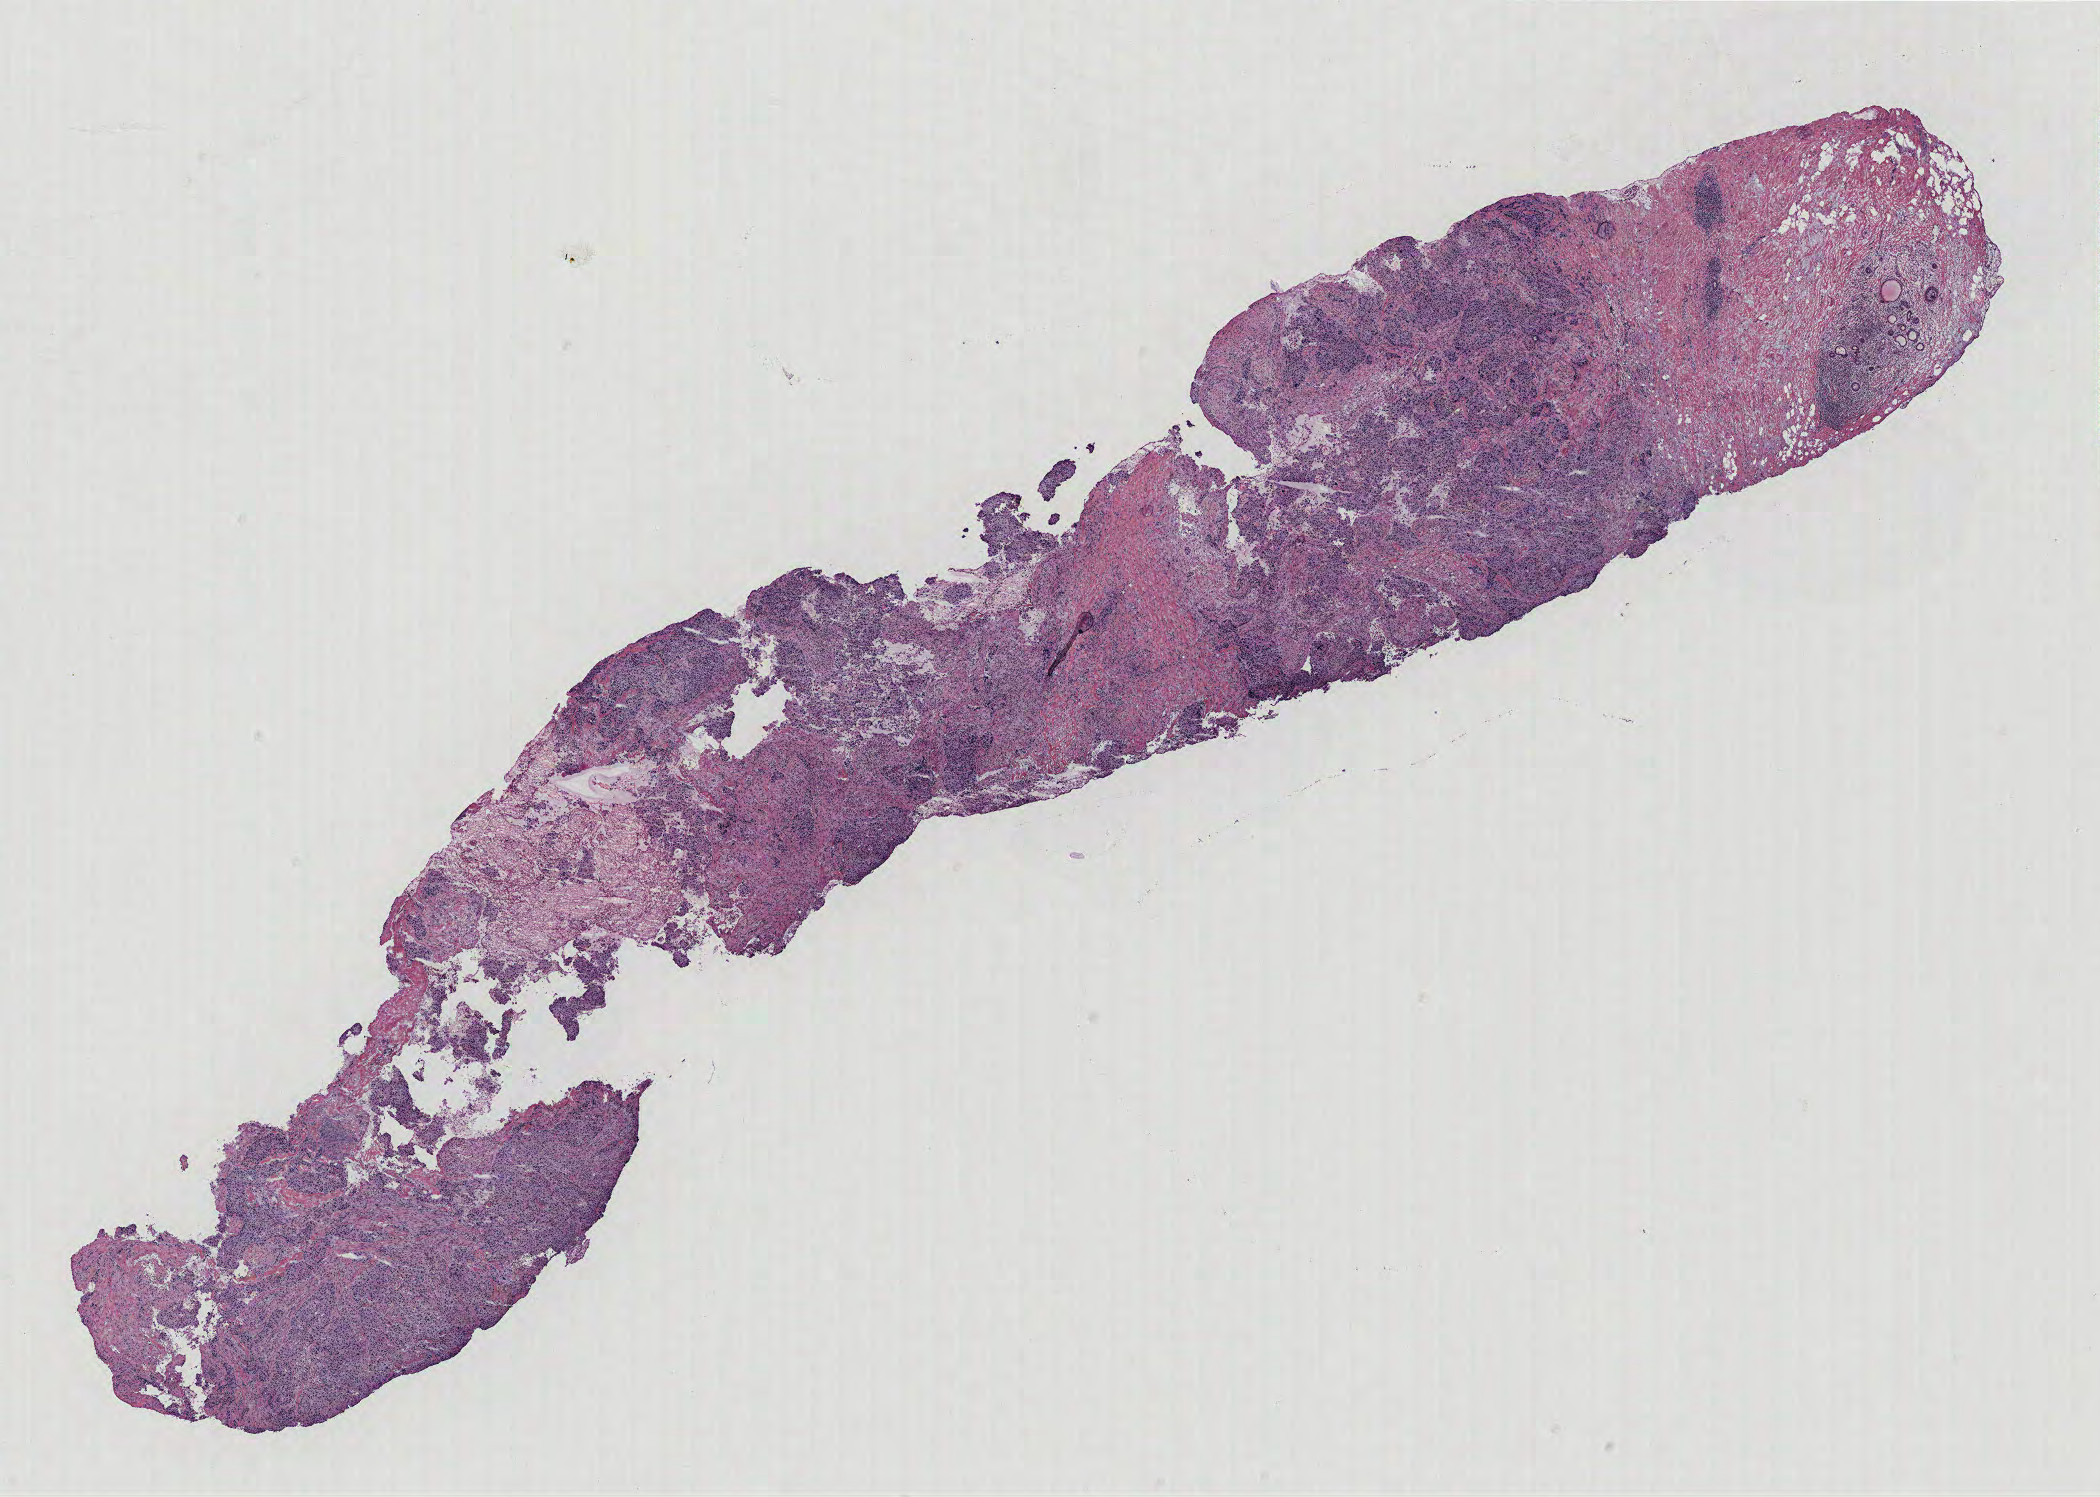
Digitized H&E-stained tissue section (whole slide), a low-resolution overview of the entire scanned area, about 16.8 x 12.0 mm, breast, tissue type not recorded. Female, 60 y/o.
- patient diagnosis: Infiltrating duct carcinoma, NOS